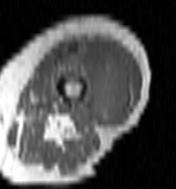
MRI of an extremity soft-tissue mass, one axial slice. Slice 39 of 100 in the series (ordered by position). MR volume resampled by the dataset authors to the PET/CT grid (not the native acquisition matrix). 176 × 189 image matrix, field of view 172 × 185 mm. Female patient. Case-level facts recorded for this patient, not image findings: histological type: undifferentiated – high grade; grade: high; site of the primary tumour: left thigh.
Annotated regions visible in this slice (expert contour drawn on MRI and transferred to this co-registered scan by the dataset authors):
- gross tumour volume including surrounding oedema: bounding box (x1, y1, x2, y2) in pixels: (60, 45, 131, 126)
- gross tumour volume (mass): (82, 47, 131, 126)